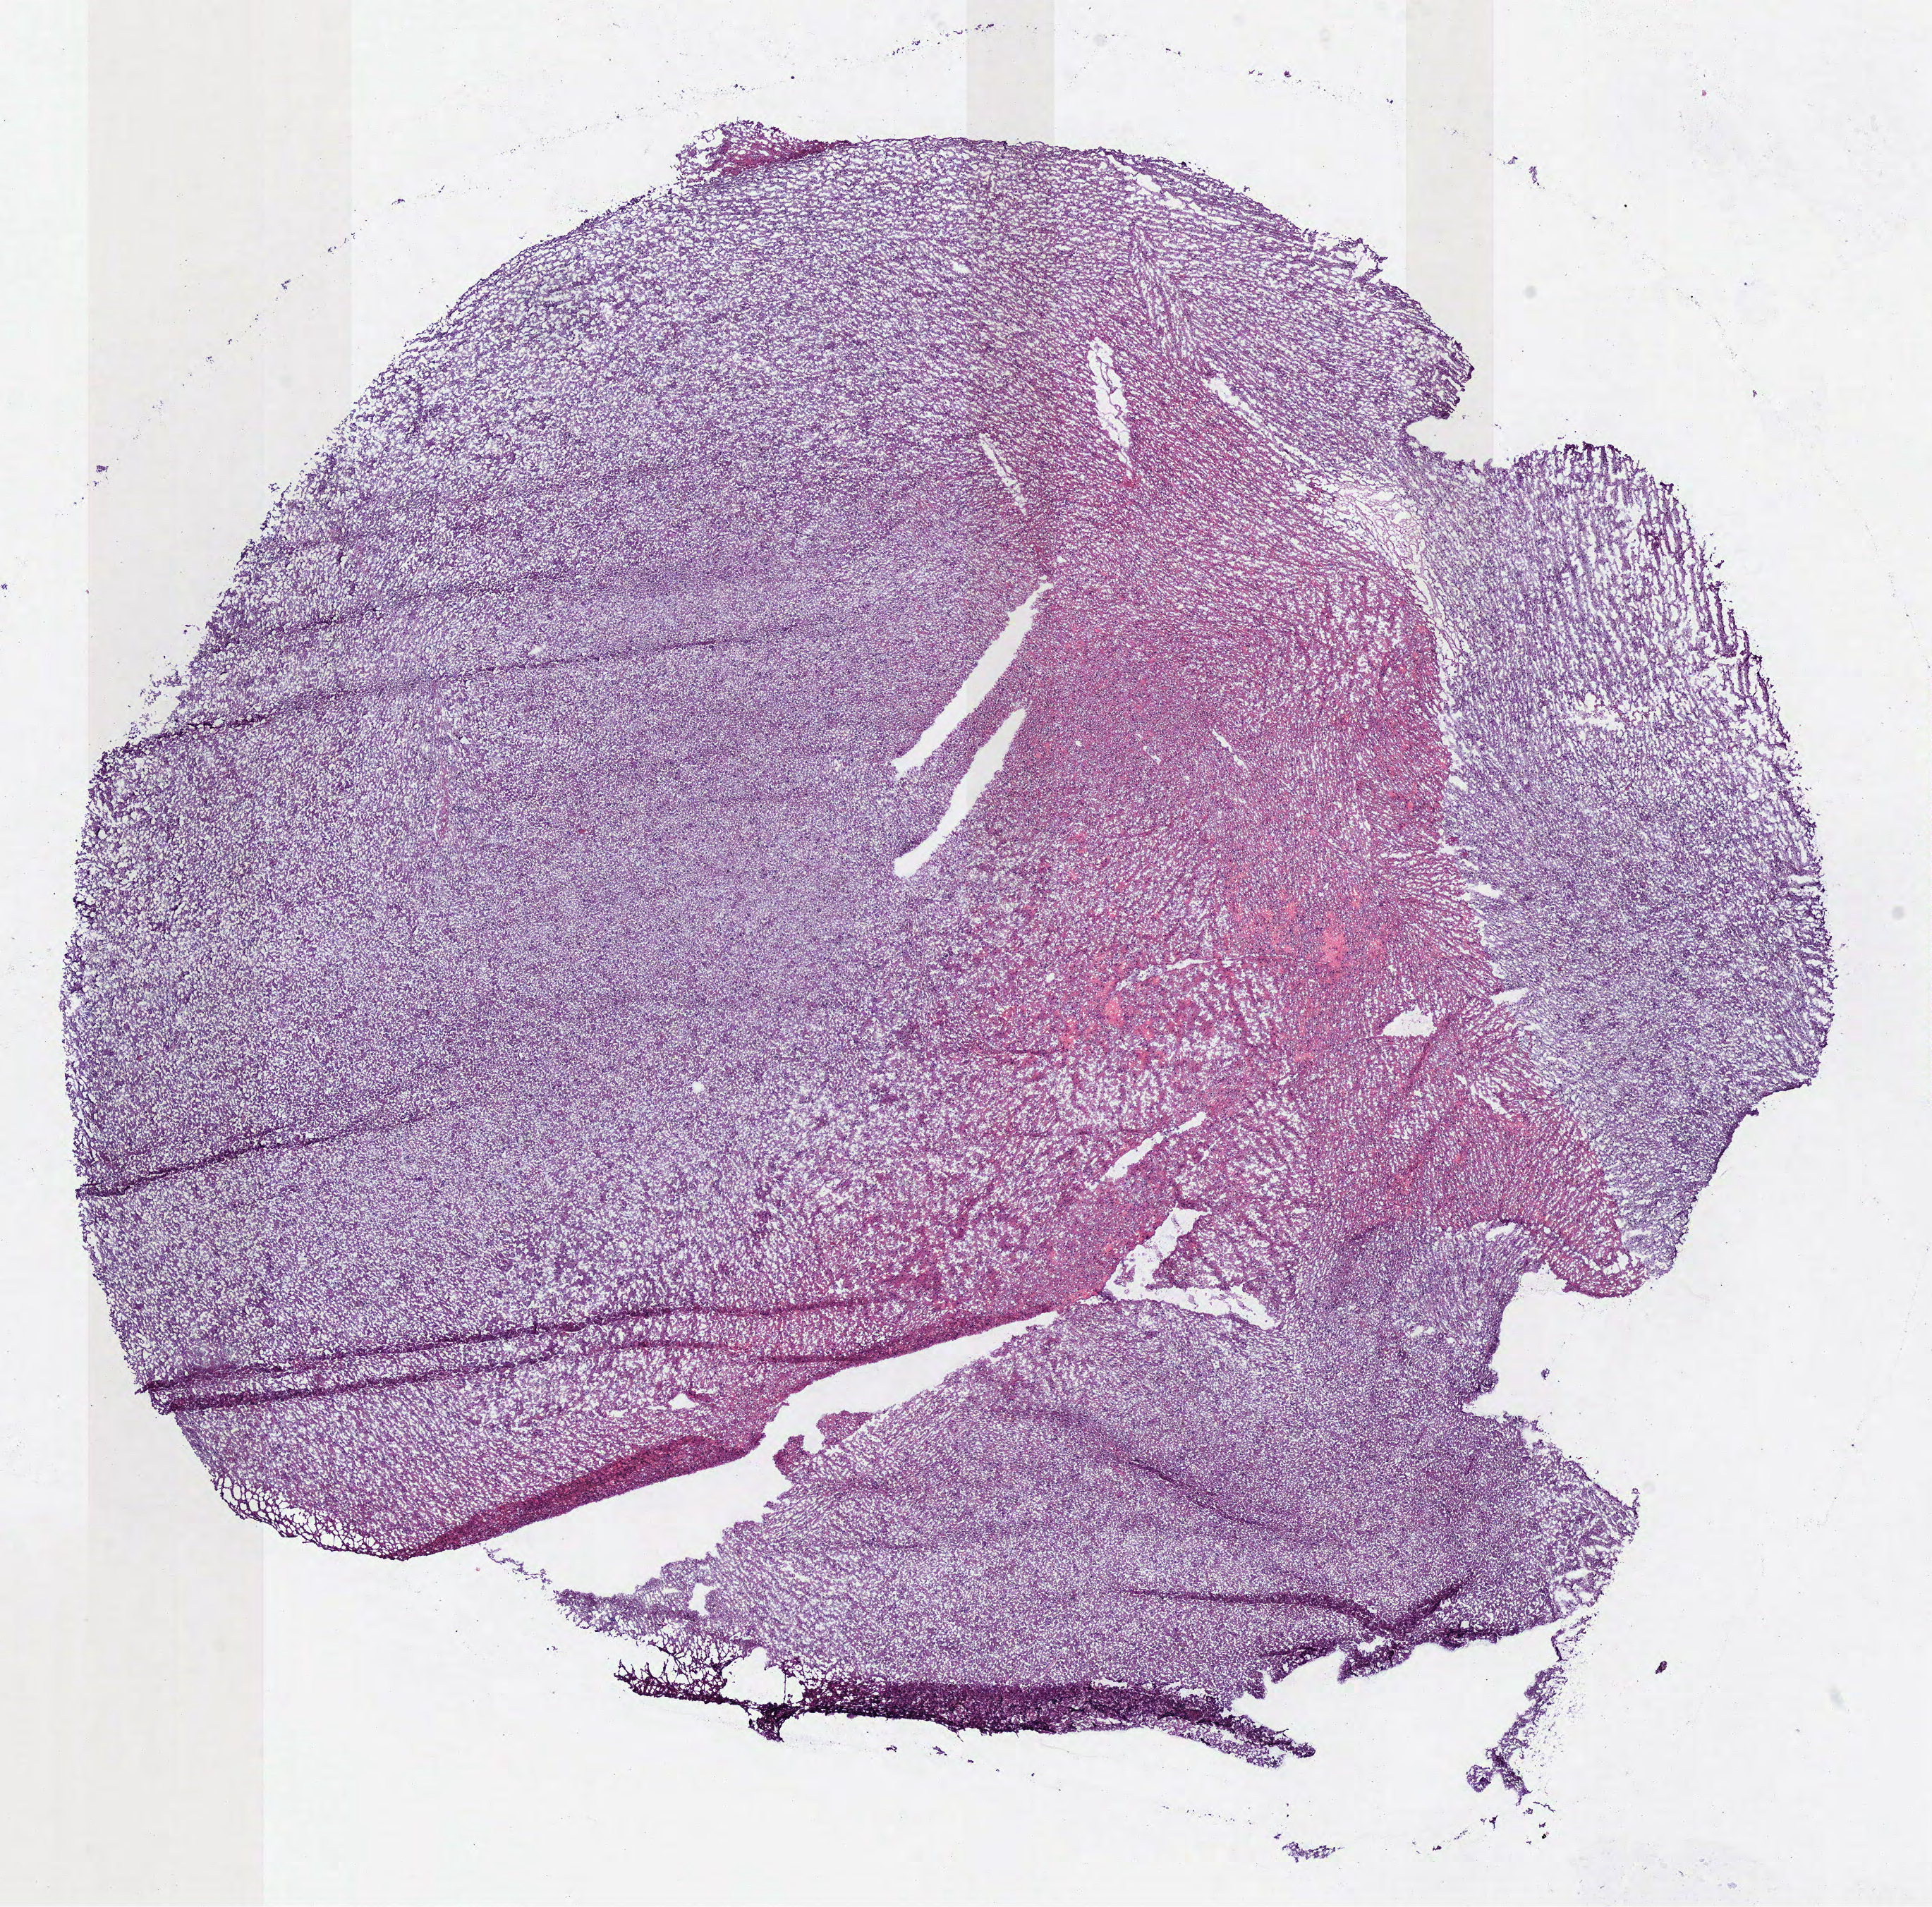
Whole-slide histology image, H&E — whole scanned area (about 10.8 x 10.6 mm, from a 40x scan) shown as a low-resolution overview. Frozen section. Primary tumour sample from the brain. Patient: female, age at initial diagnosis 32 years. Histologic grade: G2 (moderately differentiated). Composition of this section per pathologist review: tumour cells 100%, tumour nuclei 70%, normal cells 0%, stromal cells 0%, necrosis 0%.
Diagnosis: Oligodendroglioma, NOS (cerebrum). Laterality: left.